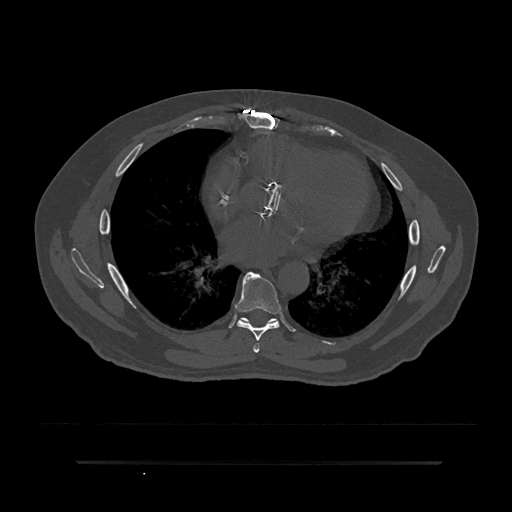
CT including the spine, one axial slice. Slice 468 of 797 in the series (ordered by position). Reconstruction kernel Br40s/3. 120 kVp. Bone window (W 1800 / L 400 HU). 0.5 mm slice thickness. 512 × 512 image matrix, field of view 464 × 464 mm. Patient: male, 59 years. Case-level facts recorded for this patient, not image findings: primary cancer: bile ducts; vertebrae with lytic lesions (as recorded): T10.
Structures marked on this image (semi-automatic segmentation, software-assisted and operator-edited):
- T6 vertebra: box from (x=253, y=343) to (x=260, y=353) px
- T7 vertebra: (x=235, y=272)–(x=281, y=341)
- T8 vertebra: (x=239, y=317)–(x=295, y=332)